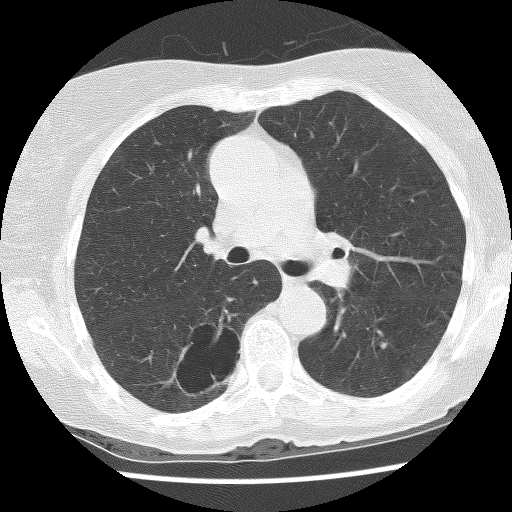
Low-dose screening chest CT, axial slice; baseline screening round; lung window (W 1500 / L -600 HU); 120 kVp; slice 51 of 136 in the series; 512 × 512 image matrix, field of view 300 × 300 mm. Female participant, aged 69 years at enrolment. Former smoker at enrolment.
Lesion marked by an expert reader, box from (x=160, y=320) to (x=246, y=395) px. The screening reader recorded 2 non-calcified nodules or masses ≥4 mm on this exam (right lower lobe, right lower lobe); which of them this box marks is not recorded. Later outcome: lung cancer diagnosed 288 days after this screen — non-small cell carcinoma, right lower lobe, poorly differentiated (G3), stage IB (AJCC 6th edition), 36 mm at pathology.